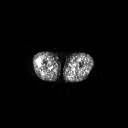
FDG PET of an extremity soft-tissue mass (from a PET/CT study), one axial slice; position 218 of 267 along the scan axis; 3.27 mm slice thickness; 128 × 128 image matrix, field of view 700 × 700 mm. Patient: male, 43 years. Case-level facts recorded for this patient, not image findings: histological type: poorly differentiated synovial sarcoma; grade: high; site of the primary tumour: right buttock.
Outlined on this slice (expert contour drawn on MRI and transferred to this co-registered scan by the dataset authors):
- gross tumour volume including surrounding oedema: bounding box <37,60,42,66> (left, top, right, bottom; pixels)